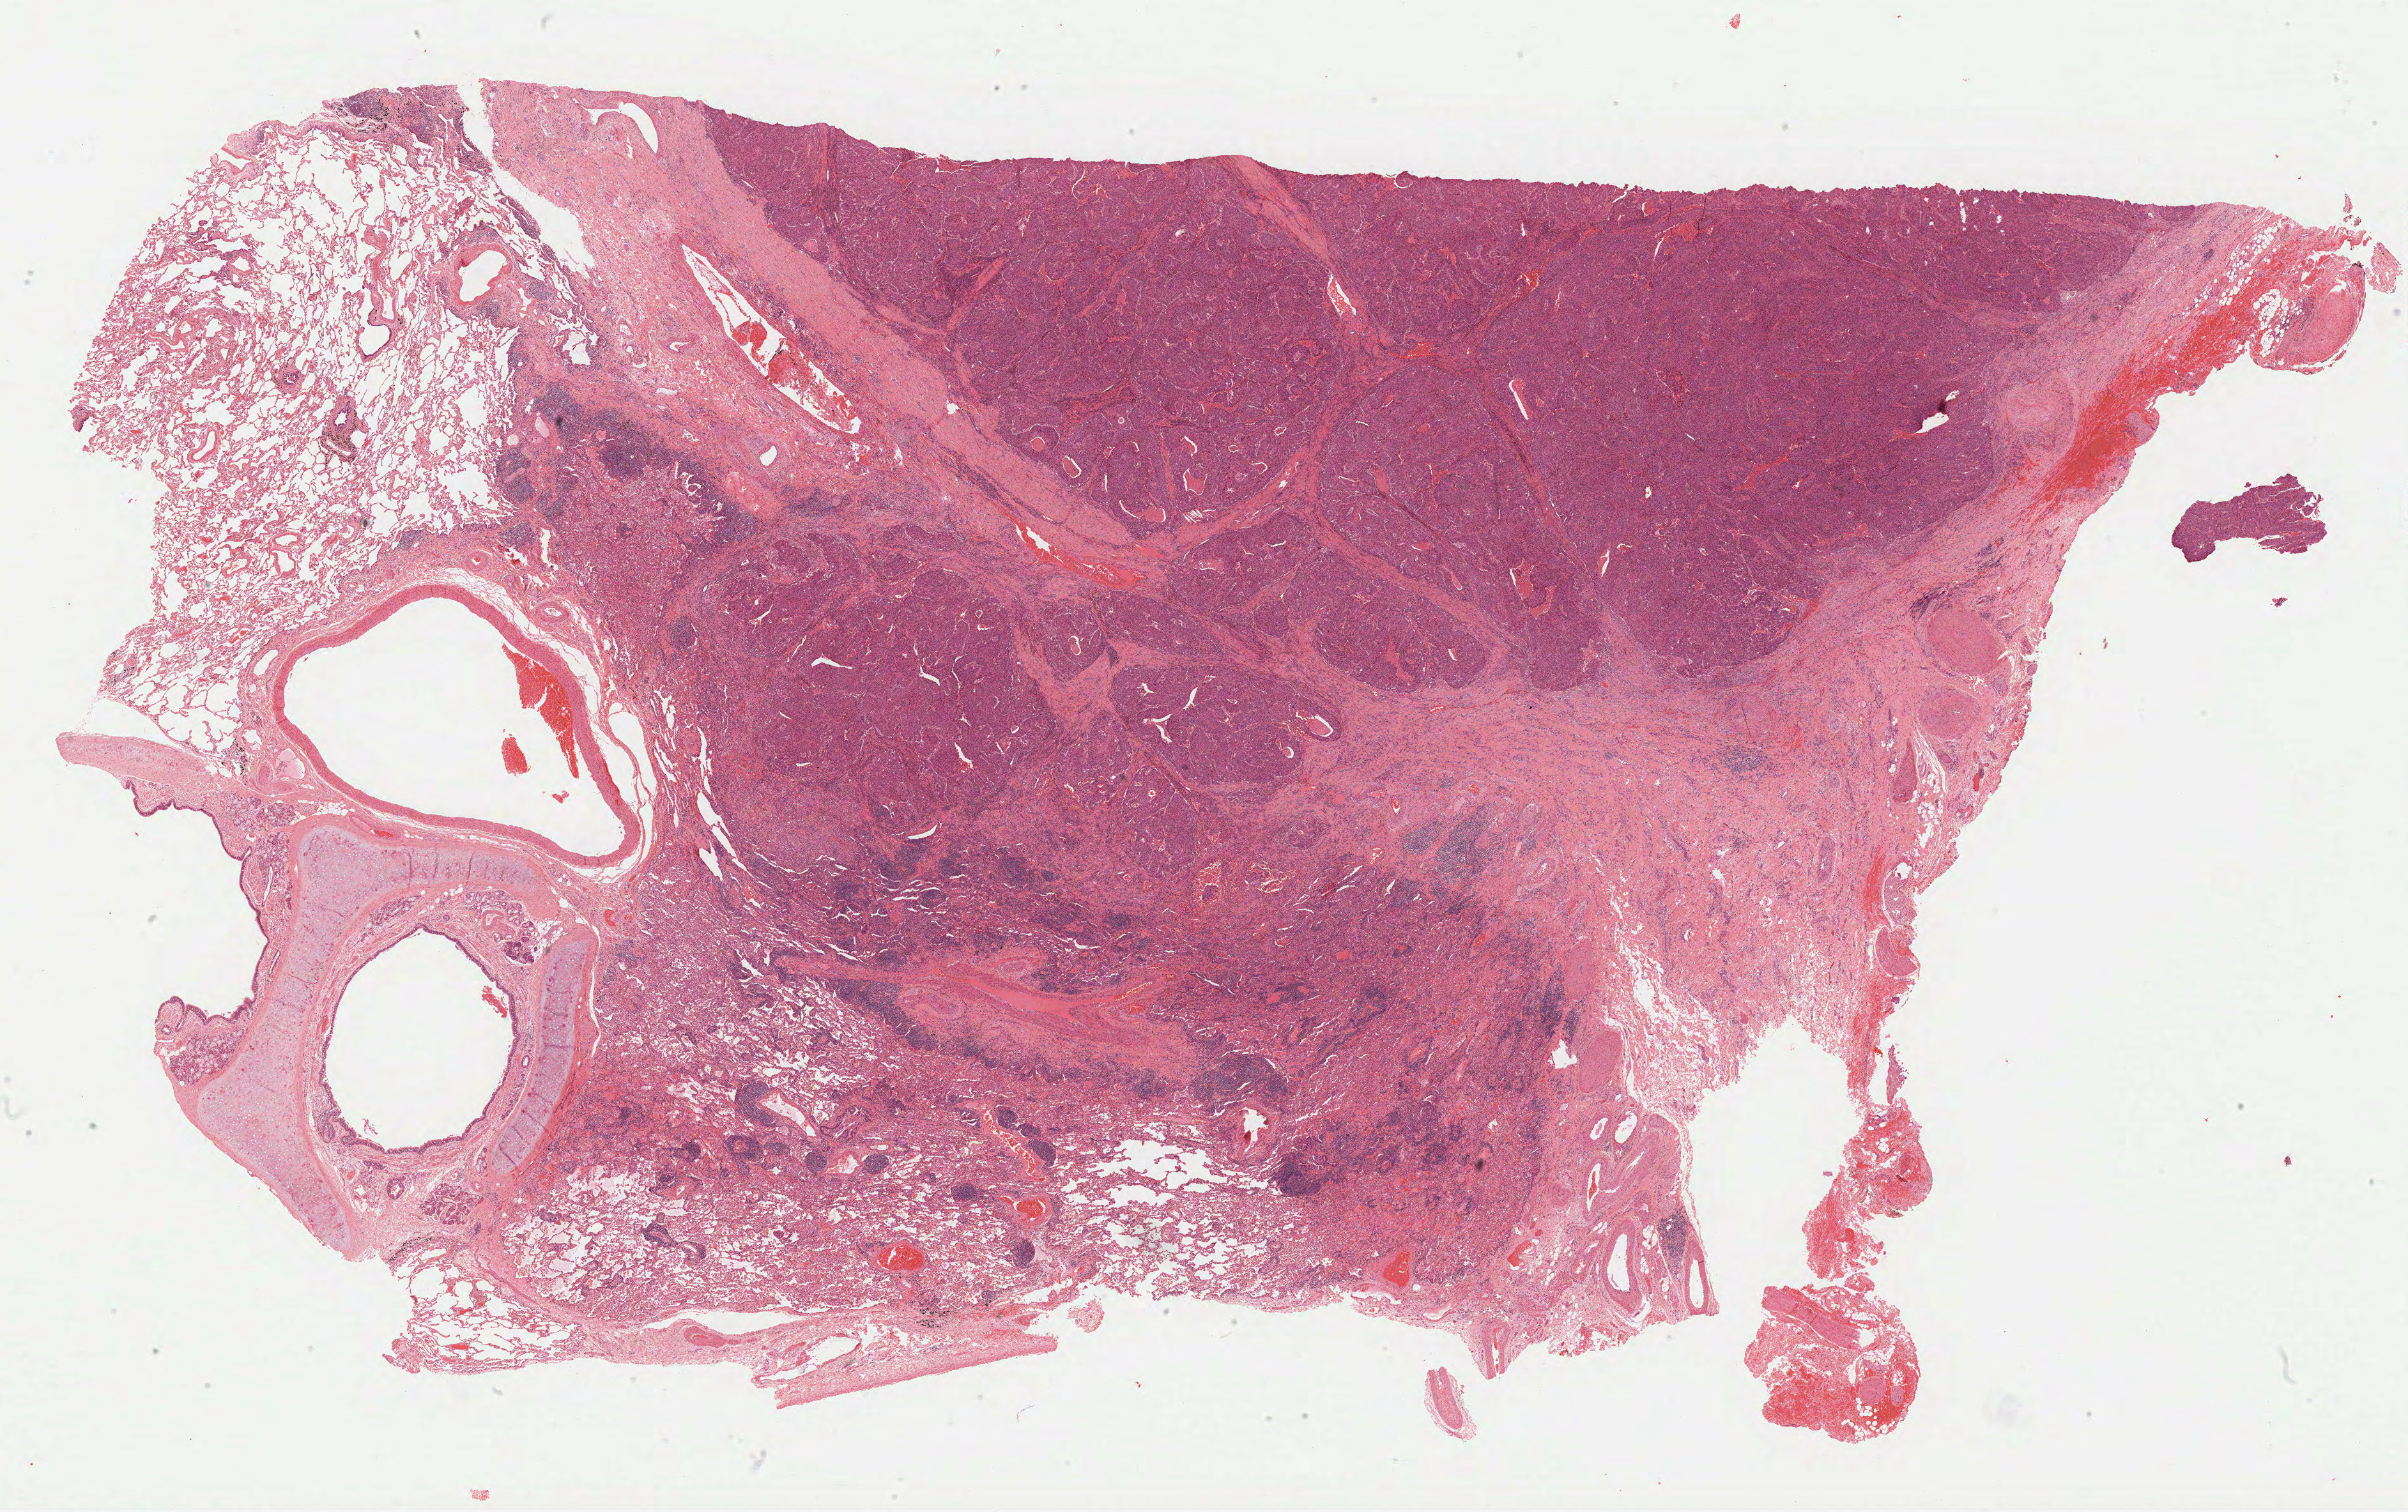
Whole-slide histology image, H&E-stained — whole scanned area (about 30.4 x 19.1 mm) shown as a low-resolution overview. Formalin-fixed paraffin-embedded (FFPE) diagnostic section. Primary tumour sample from the lung. Patient: male, age at initial diagnosis 57 years.
Diagnosis: Squamous cell carcinoma, NOS.